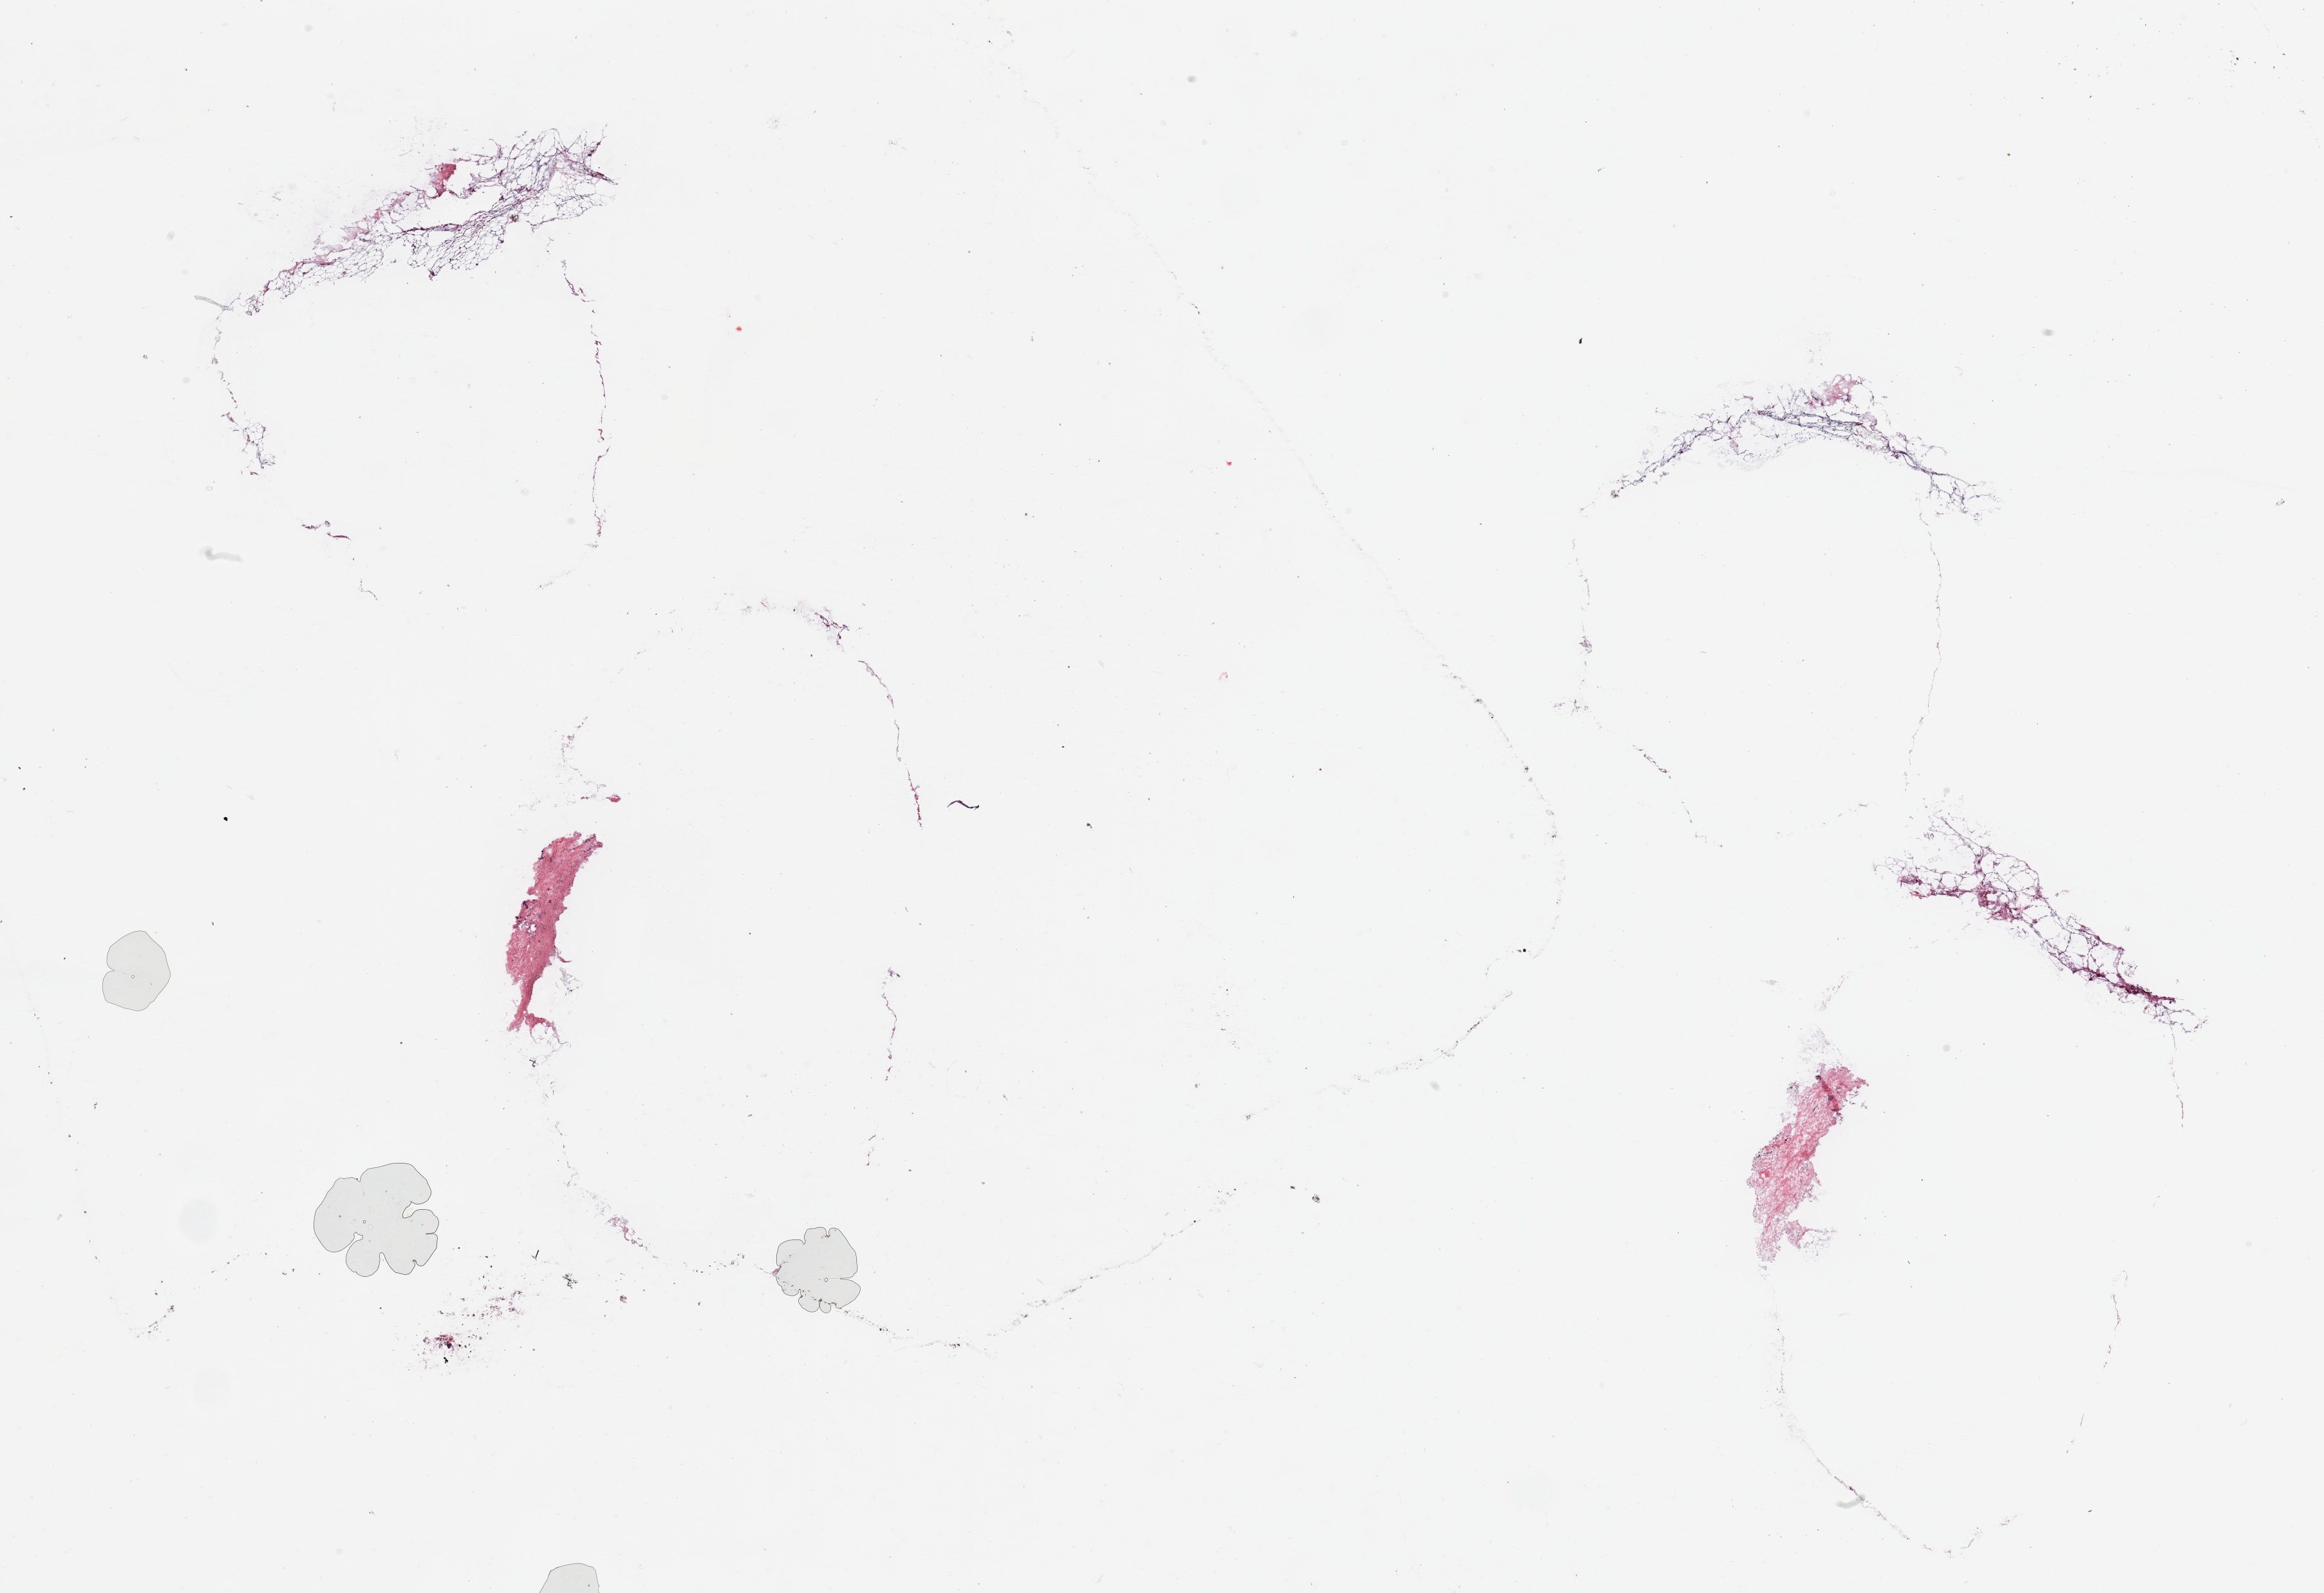
Digitized H&E-stained tissue section (whole slide) — a low-resolution overview of the entire scanned area, about 28.5 x 19.6 mm; tumour tissue sample, breast. Patient: female, age 35 years.
AJCC pathologic stage: IIB. Histologic diagnosis: Infiltrating duct carcinoma, NOS.